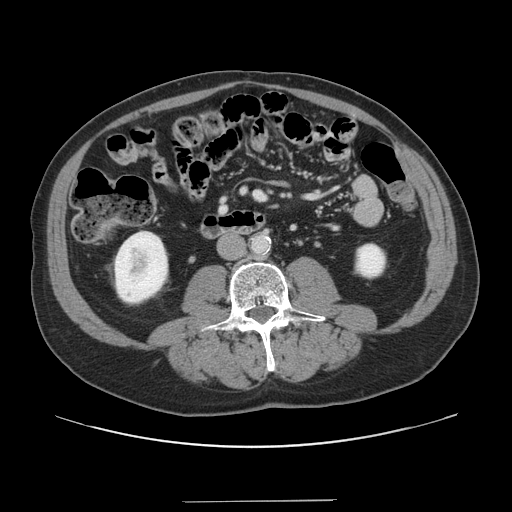
Contrast-enhanced abdominal CT, one axial slice; slice 27 of 151 in the series (ordered by position); 120 kVp; intravenous contrast given; soft-tissue window (W 400 / L 40 HU); 2.5 mm slice thickness; 512 × 512 image matrix. Male patient, age 63 years. From the clinical record (not read from this slice): diagnosis: colorectal cancer liver metastases, imaged before liver resection; multiple liver metastases: no.
Structures marked on this image (outlined manually by an expert reader):
- portal vein (with intrahepatic branches): bounding box (x1, y1, x2, y2) in pixels: (254, 192, 265, 199)